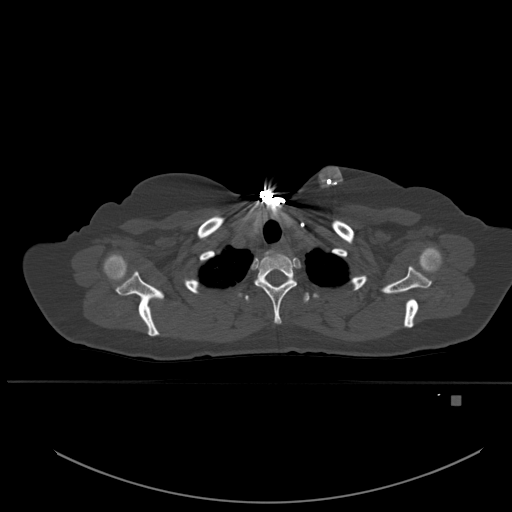
CT including the spine, one axial slice. Slice 417 of 651 in the series (ordered by position). Bone window (W 1800 / L 400 HU). 1.5 mm slice thickness. 512 × 512 image matrix, field of view 443 × 443 mm. Patient: female, 49 years. From the clinical record (not read from this slice): primary cancer: breast; vertebrae with lytic lesions (as recorded): L3, T12, L4.
Structures marked on this image (semi-automatically segmented with operator editing):
- T1 vertebra: bounding box [x1, y1, x2, y2] px = [255, 253, 297, 324]
- T2 vertebra: [245, 292, 310, 303]